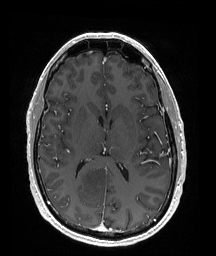
Brain MRI from a brain-tumour surgery series, one axial slice; position 88 of 176 along the scan axis; T1-weighted post-contrast; 216 × 256 image matrix, field of view 211 × 250 mm. From the clinical record (not read from this slice): histopathology: Oligodendroglioma; WHO grade: 2; IDH mutation: yes; tumour location: Right Parietal.
Annotated regions visible in this slice (outlined manually by an expert reader):
- tumour: bounding box [x1, y1, x2, y2] px = [70, 164, 111, 203]